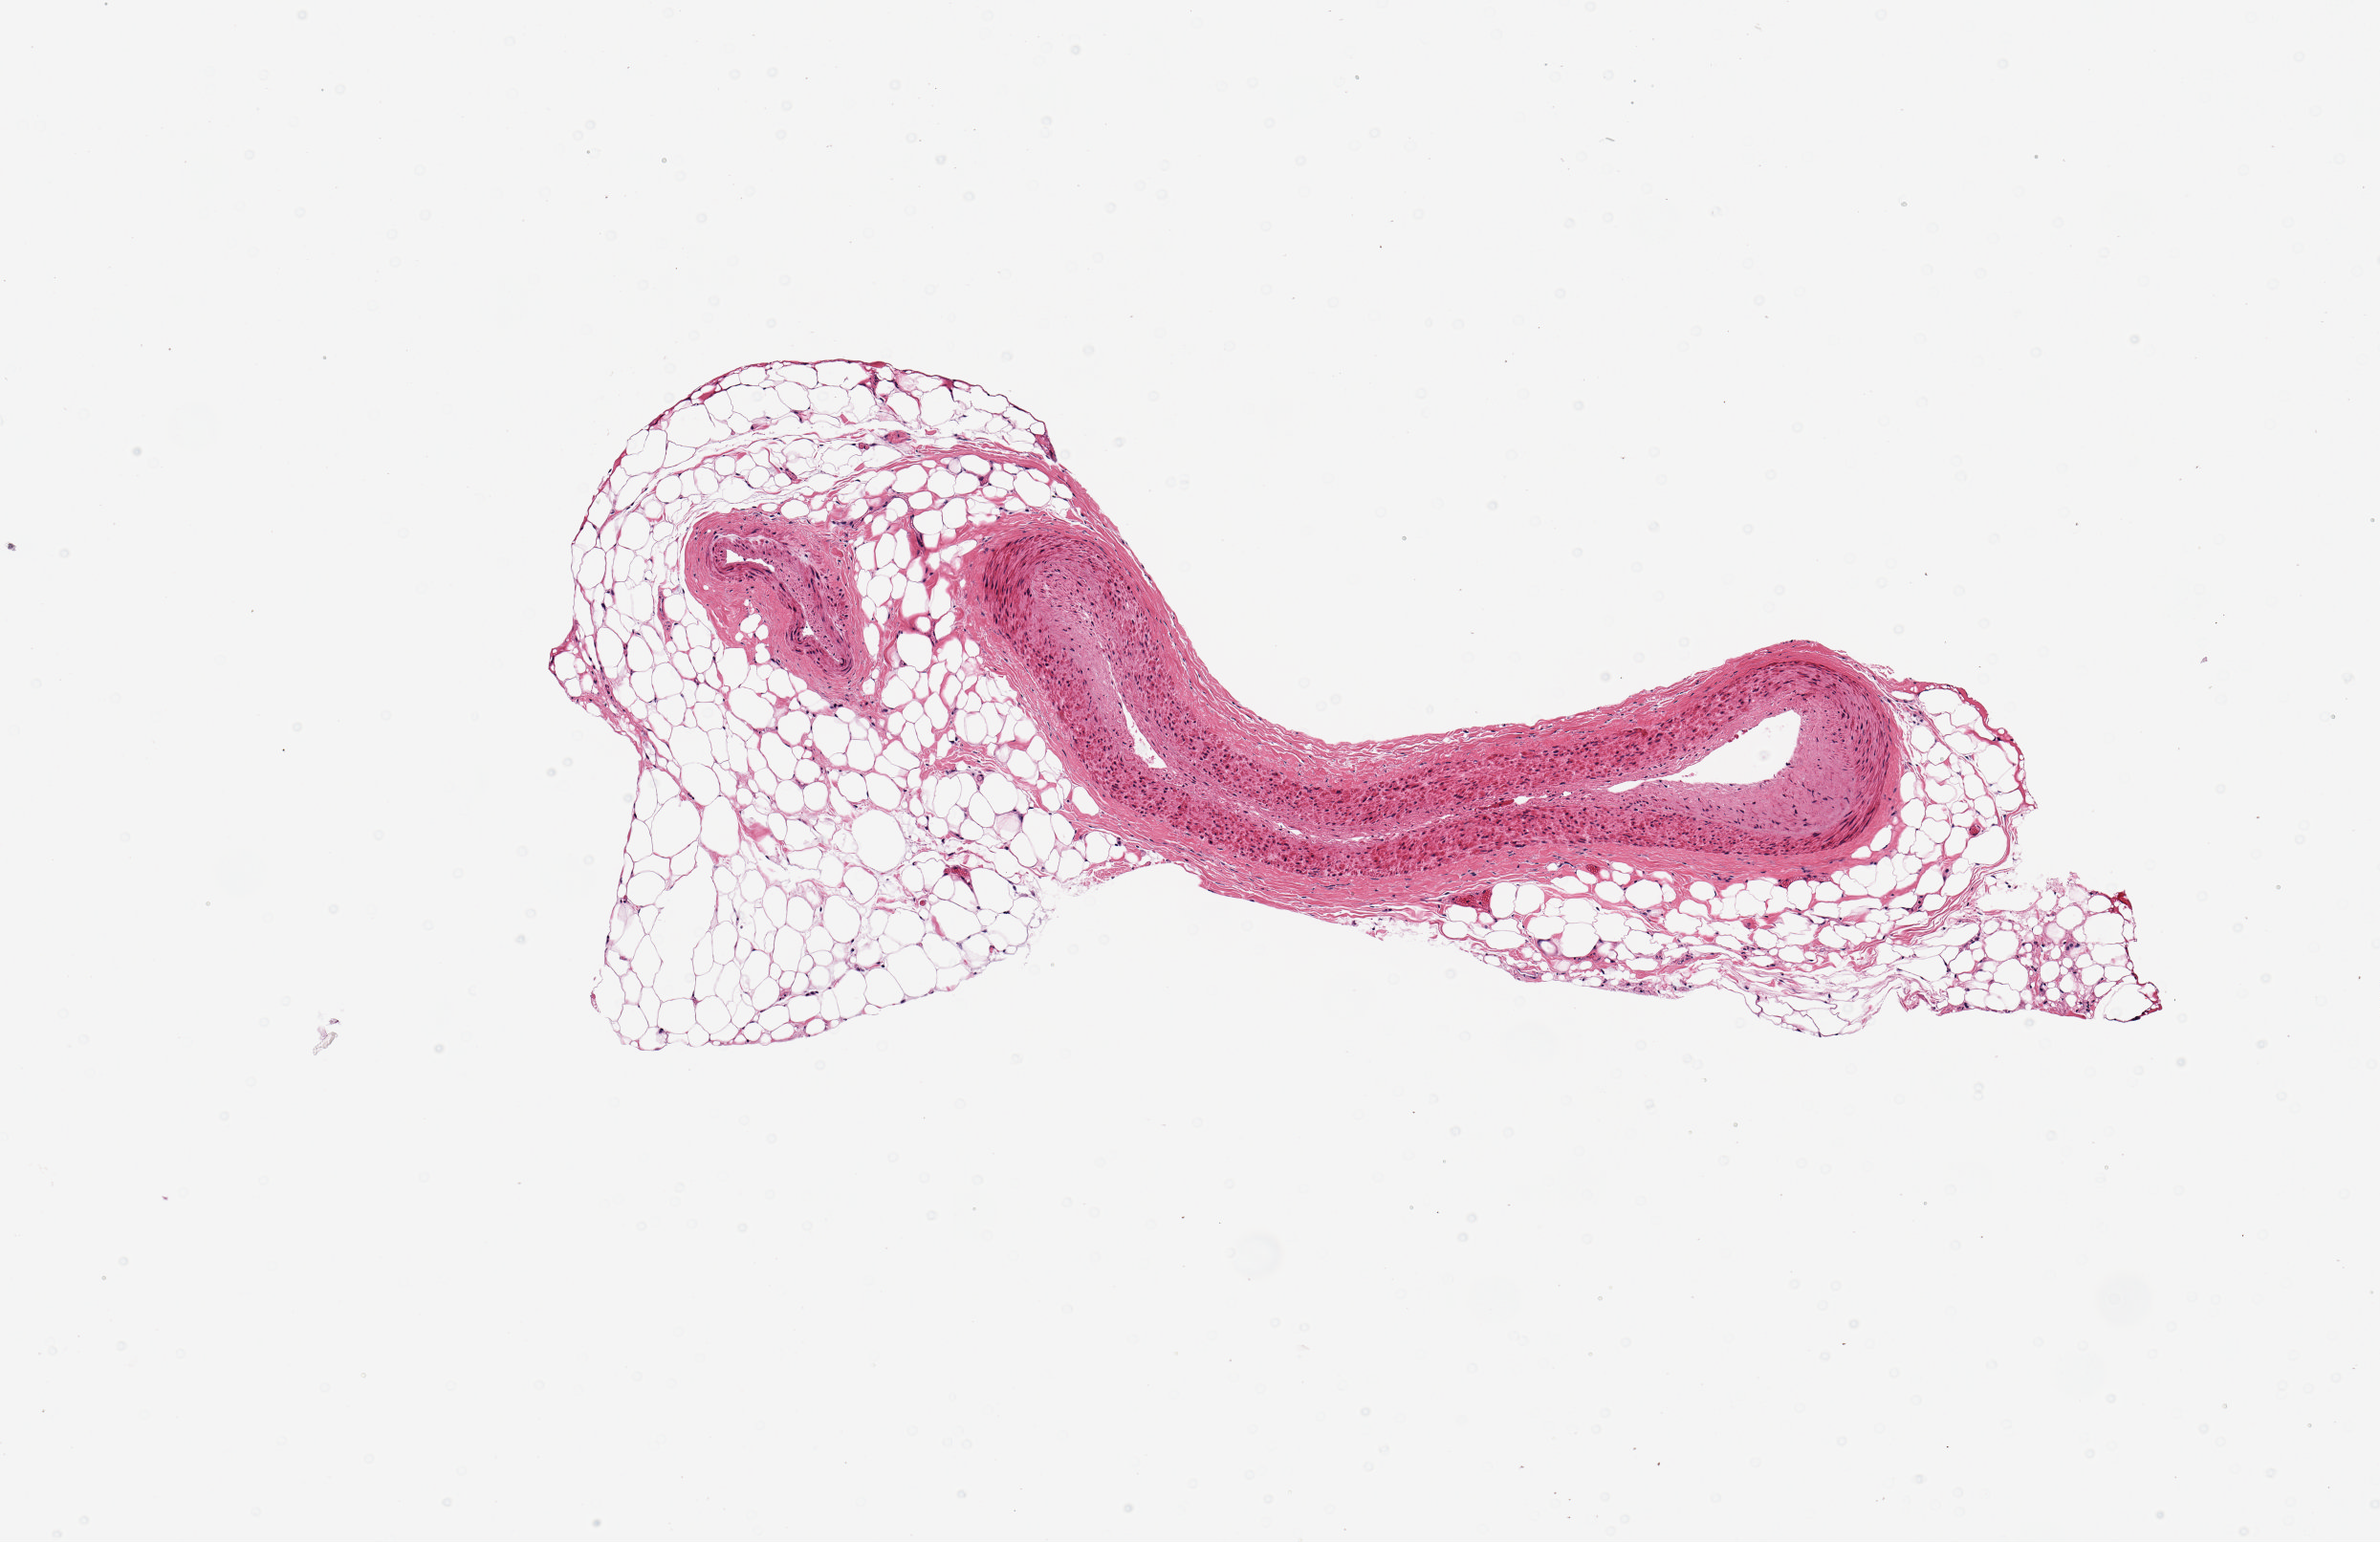
Digitized haematoxylin and eosin-stained section, a low-resolution overview of the entire scanned area, about 4.9 x 3.2 mm. PAXgene-fixed, paraffin-embedded tissue. Target tissue: coronary artery. Tissue donor sample. Female donor.
• review note (as recorded): 1 piece; 50% adjacent adipose tissue